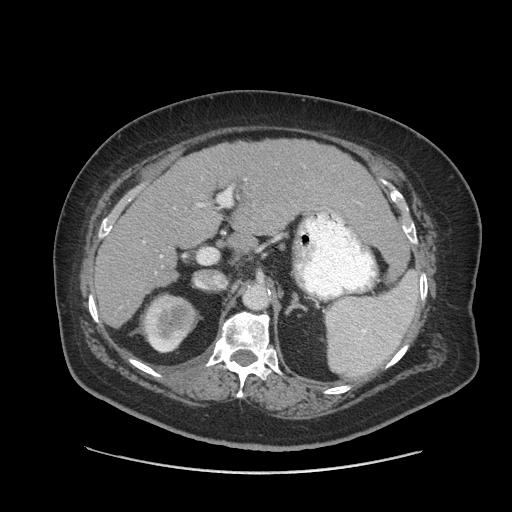
Contrast-enhanced abdominal CT (liver protocol), one axial slice; slice 48 of 91 in the series (ordered by position); reconstruction kernel STANDARD; 140 kVp; soft-tissue window (W 400 / L 40 HU); 512 × 512 image matrix, field of view 420 × 420 mm. Case-level facts recorded for this patient, not image findings: diagnosis: hepatocellular carcinoma (patient treated with transarterial chemoembolisation; whether this scan precedes or follows treatment is not stated here); TNM stage (as recorded): Stage-I.
Annotated regions visible in this slice (semi-automatically segmented with operator editing):
- liver parenchyma outside the tumour (the mass and vessels are separate outlines, so this box may not span the whole liver): bounding box <94,140,390,327> (left, top, right, bottom; pixels)
- liver vessels: <161,204,203,257>